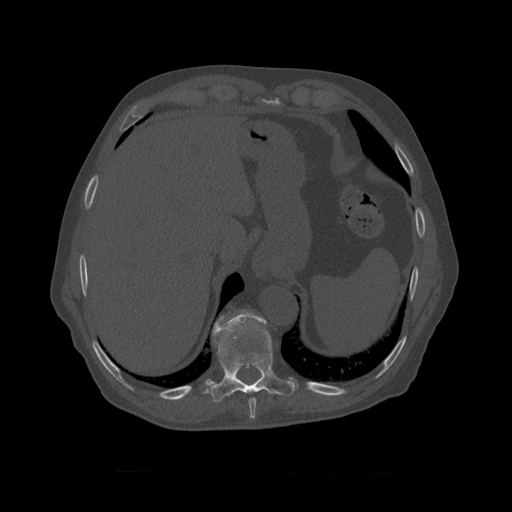
CT including the spine, one axial slice; slice 425 of 450 in the series (ordered by position); bone window (W 1800 / L 400 HU); 1.25 mm slice thickness; 512 × 512 image matrix, field of view 405 × 405 mm. Patient age 75 years. Case-level facts recorded for this patient, not image findings: primary cancer: prostate.
Structures marked on this image (semi-automatically segmented with operator editing):
- T10 vertebra: bounding box [x1, y1, x2, y2] px = [245, 310, 253, 312]
- T8 vertebra: [249, 398, 257, 411]
- T9 vertebra: [211, 311, 296, 397]